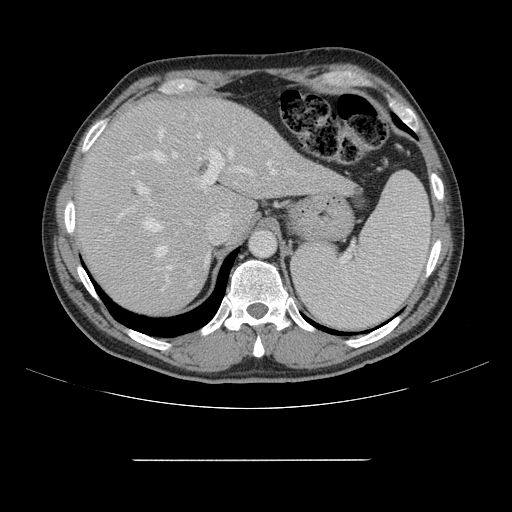
Contrast-enhanced abdominal CT, one axial slice. Position 113 of 164 along the scan axis. 120 kVp. Intravenous contrast given. Soft-tissue window (W 400 / L 40 HU). 512 × 512 image matrix, field of view 404 × 404 mm. Male patient, age 54 years. From the clinical record (not read from this slice): diagnosis: colorectal cancer liver metastases, imaged before liver resection; multiple liver metastases: yes.
Annotated regions visible in this slice (expert manual segmentation):
- hepatic veins: bounding box [x1, y1, x2, y2] px = [144, 130, 277, 280]
- liver: [77, 99, 346, 315]
- planned liver remnant (the part of the liver to remain after resection): [77, 99, 245, 315]
- portal vein (with intrahepatic branches): [118, 128, 250, 292]